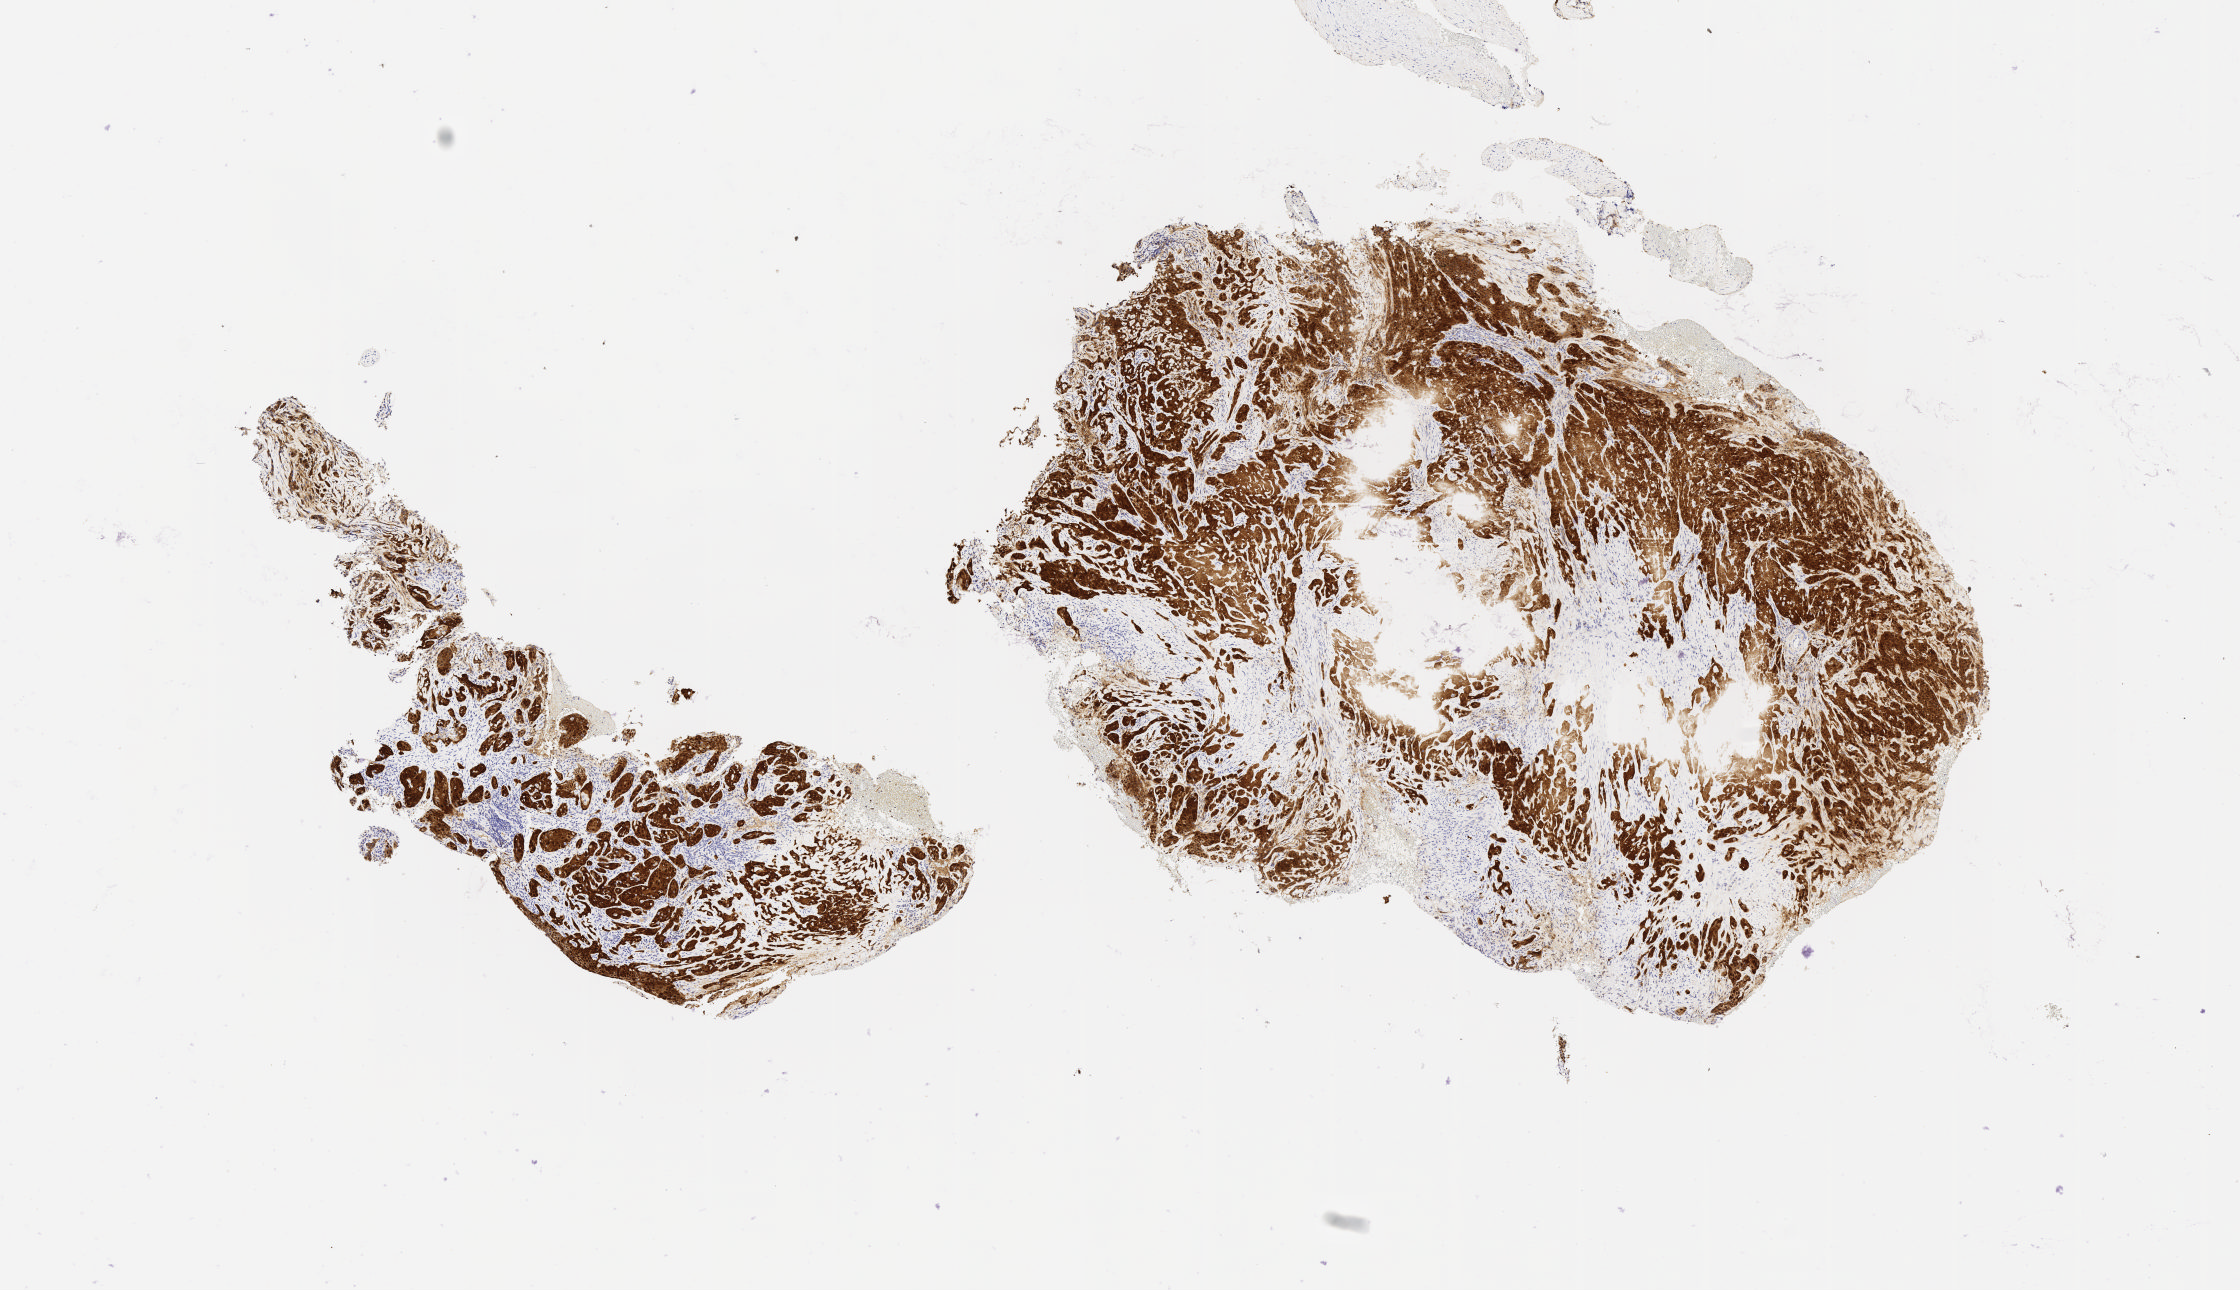
Immunohistochemistry (IHC) whole-slide image stained for p16 (p16INK4a), low-resolution overview of the scanned area, about 9.1 x 5.2 mm; tumor tissue; anatomic site: cervix. Patient female; aged 41.
Histologic diagnosis: Squamous cell carcinoma, large cell, nonkeratinizing, NOS.